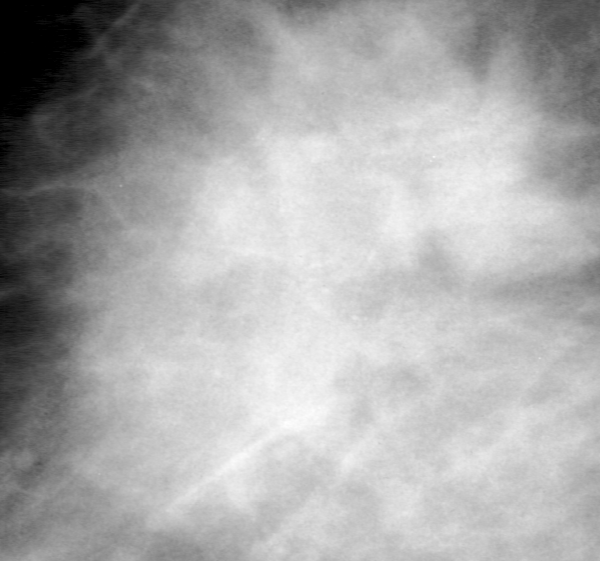
Cropped region of a digitized screen-film mammogram centred on a radiologist-marked abnormality; left breast; MLO view; BI-RADS breast density category 4 (scale 1–4).
- Marked abnormality: mass, shape irregular, margins spiculated; BI-RADS assessment category 5; pathology (as recorded): malignant.